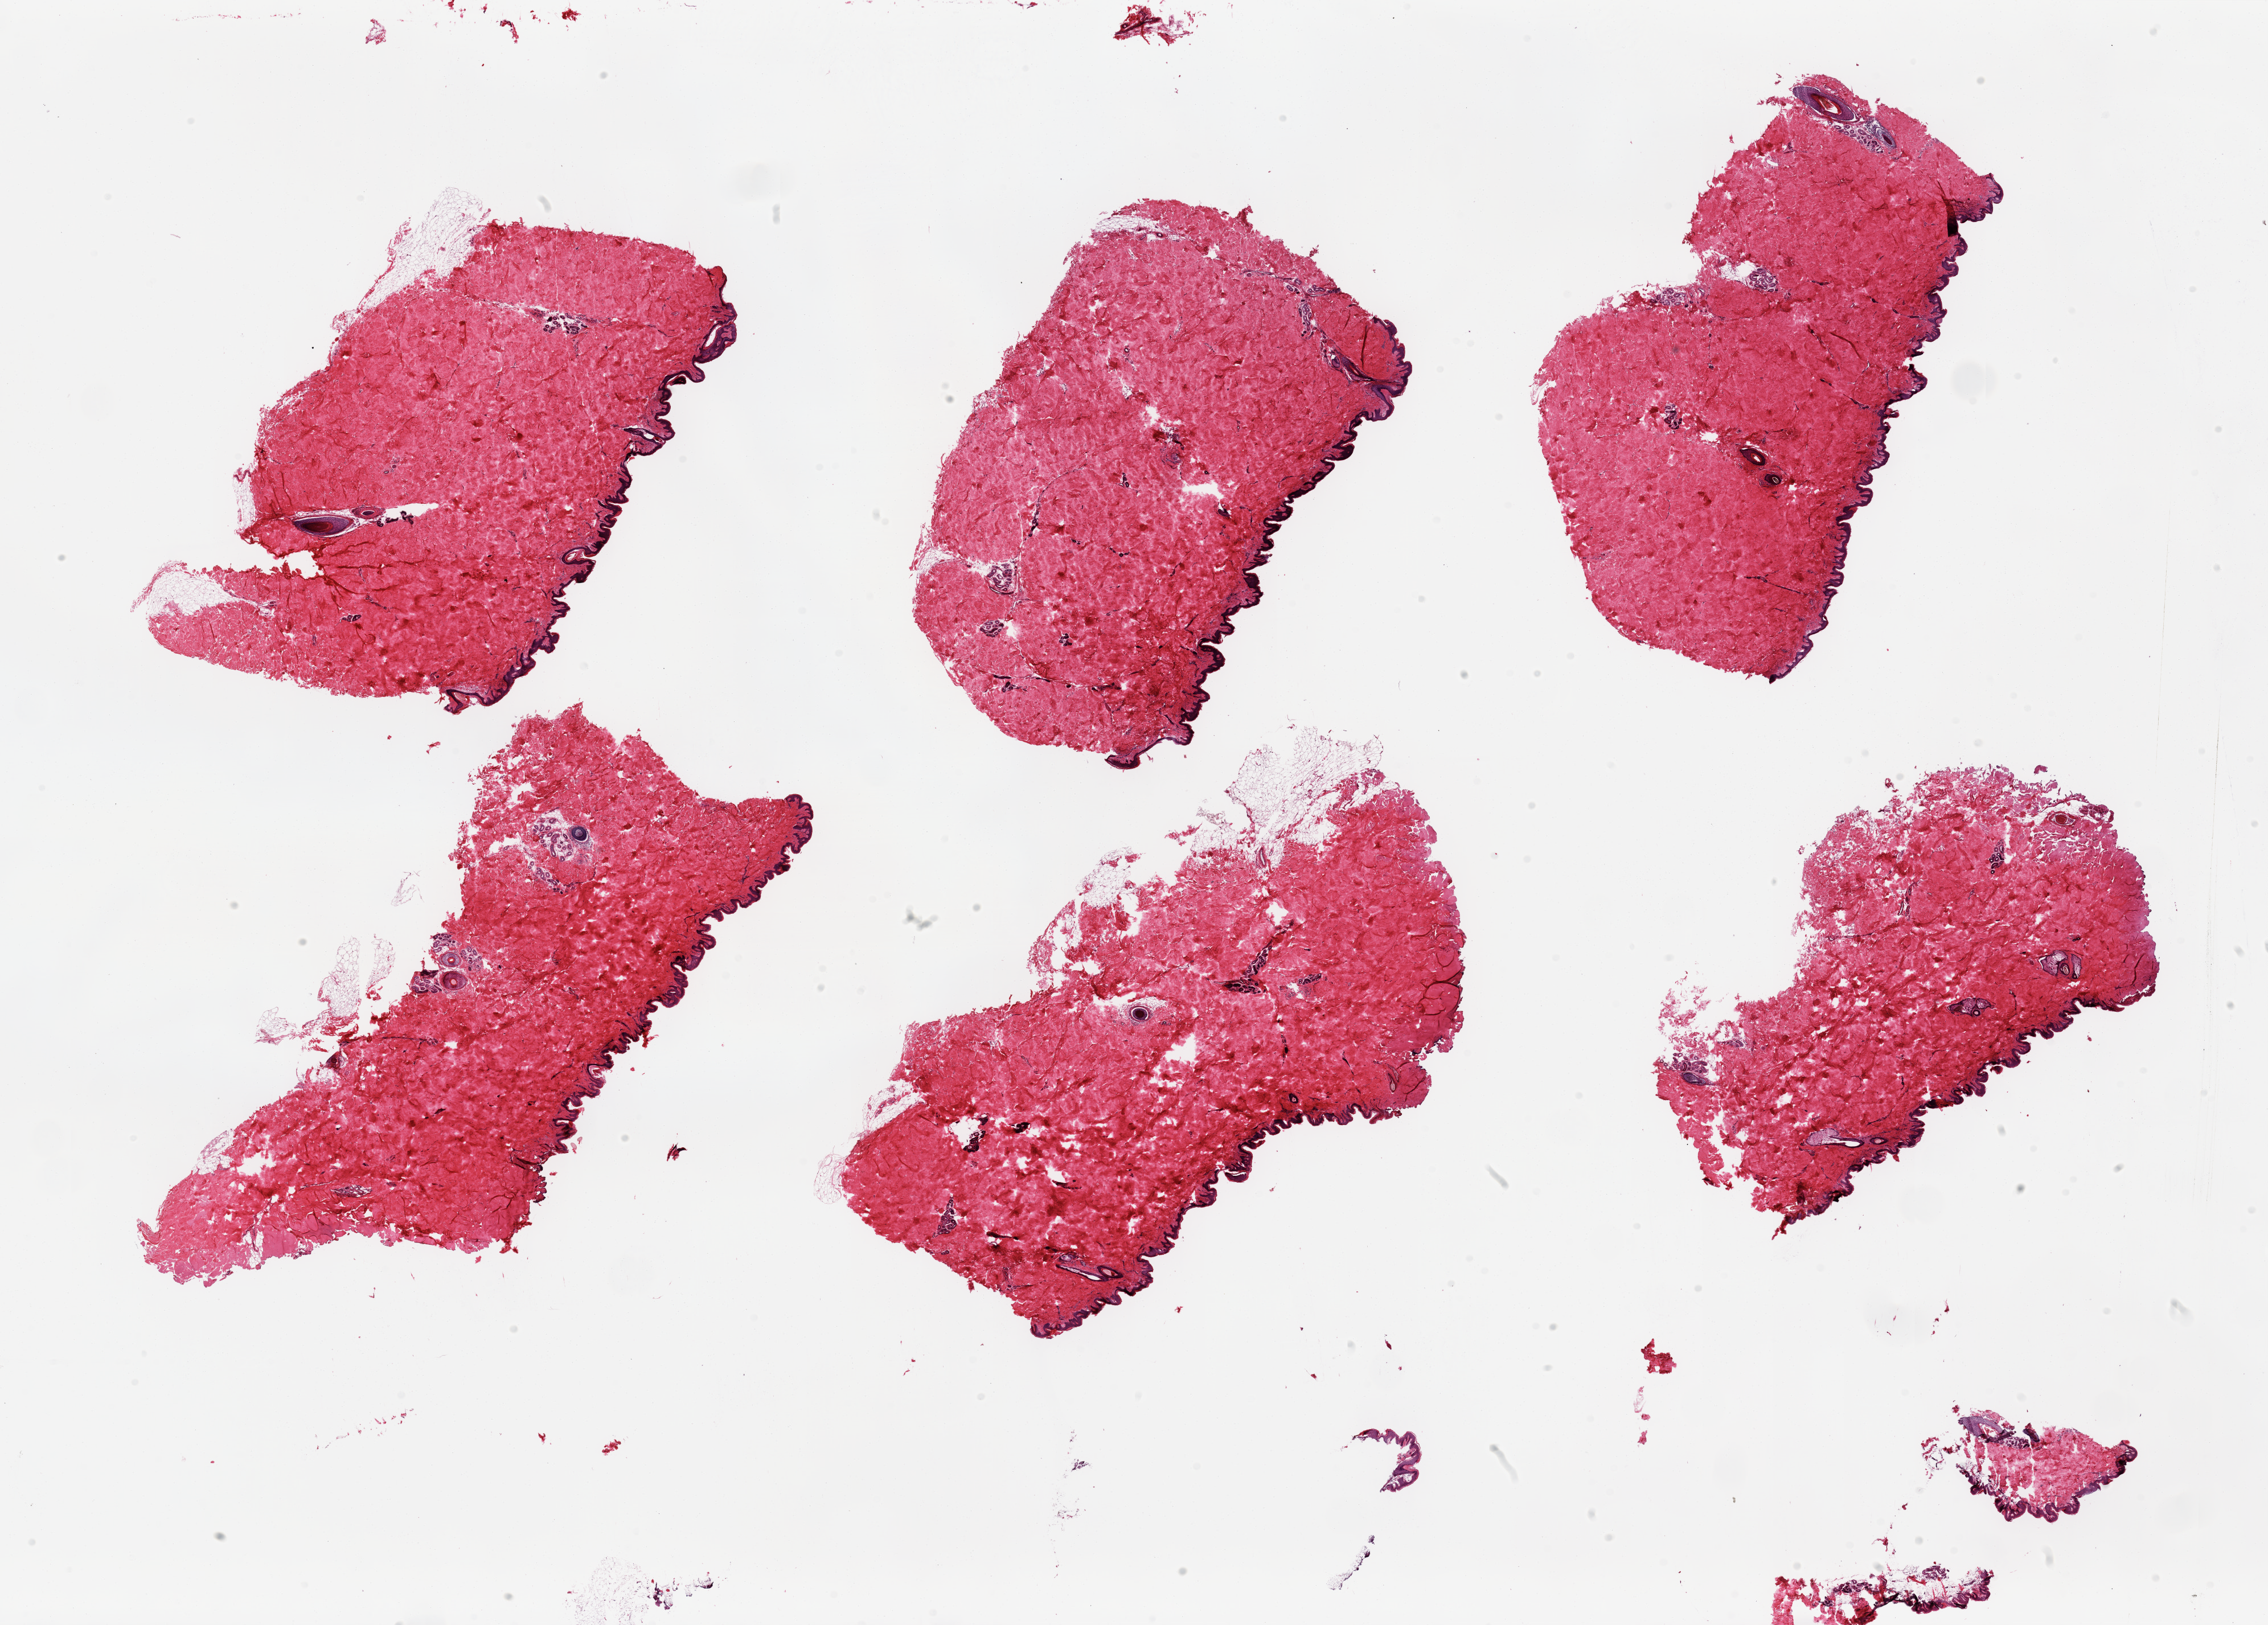
Digitized haematoxylin and eosin-stained section, brightfield — shown as a low-resolution overview of the whole scanned area (about 31.5 x 22.6 mm). PAXgene-fixed paraffin-embedded (PFPE) section. Sampled site (target tissue): skin of suprapubic region. Donor tissue sample.
Pathologist's review note for this sample: 6 pieces; predominantly well trimmed with only small attachments of residual fat.